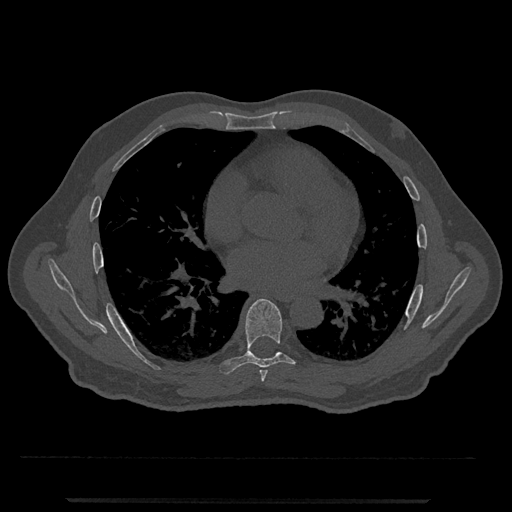
CT including the spine, one axial slice. Position 688 of 797 along the scan axis. Reconstruction kernel Br40s/3. Bone window (W 1800 / L 400 HU). 0.5 mm slice thickness. 512 × 512 image matrix, field of view 419 × 419 mm. Patient: male, 63 years. Case-level facts recorded for this patient, not image findings: primary cancer: prostate.
Structures marked on this image (semi-automatically segmented with operator editing):
- T6 vertebra: bounding box [x1, y1, x2, y2] px = [259, 370, 268, 382]
- T7 vertebra: [219, 299, 295, 375]